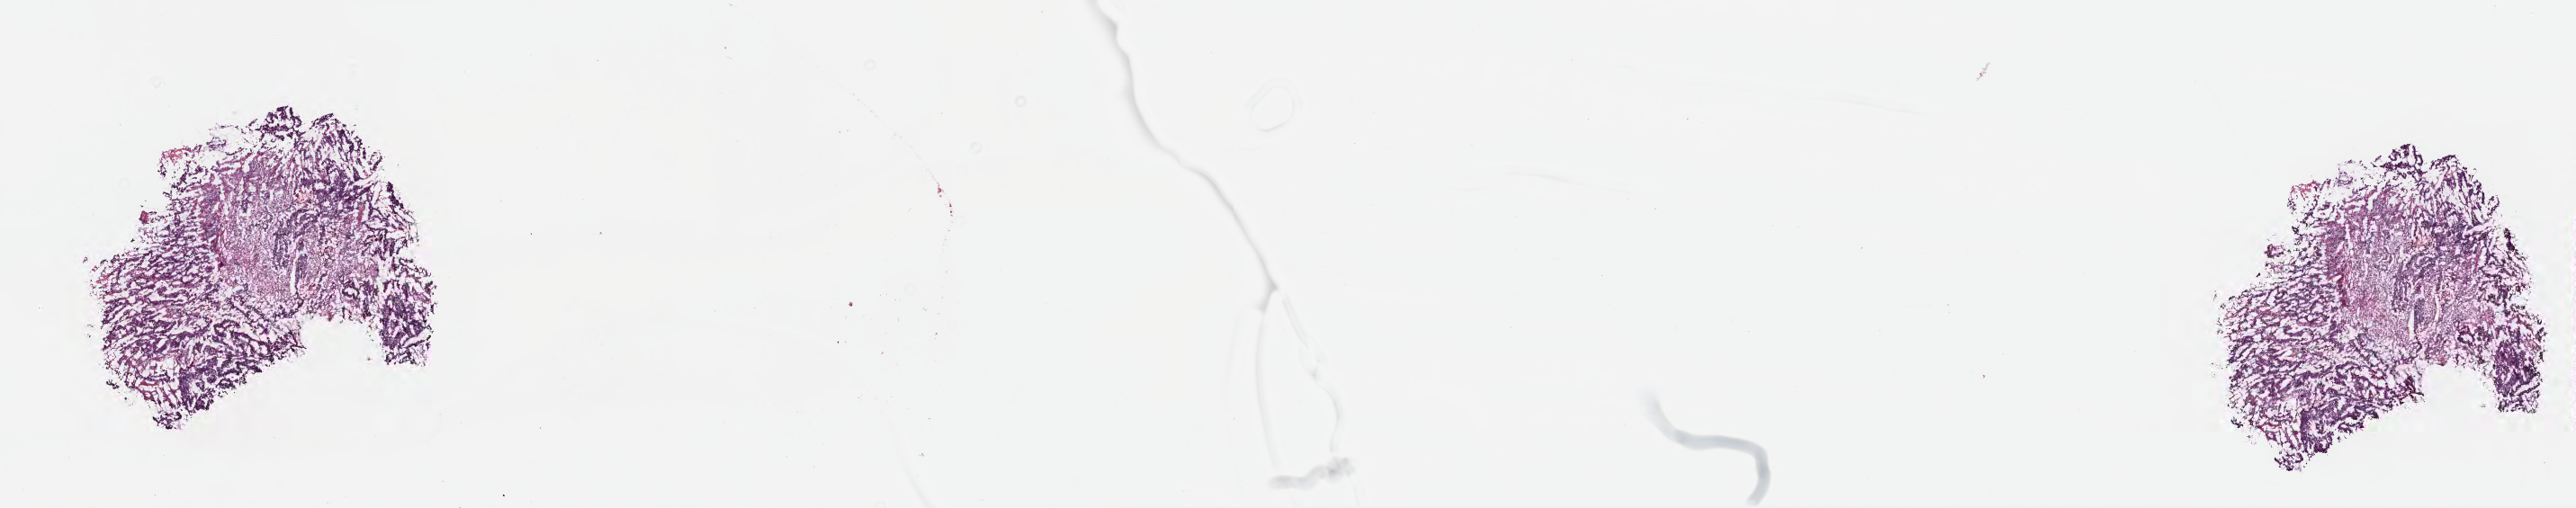
Digitized H&E-stained section — whole scanned area (about 23.1 x 4.6 mm) shown as a low-resolution overview, frozen section (tissue freezing medium), metastatic tumor tissue. Female patient; age at initial diagnosis 63 years. Composition of this section per pathologist review: tumor cells 70%, tumor nuclei 70%, stromal cells 20%, necrosis 0%, normal cells 10%. Inflammatory infiltration, as recorded: lymphocyte infiltration 8%, monocyte infiltration 0%, neutrophil infiltration 2%.
Section: bottom of the tissue portion. Patient diagnosis (primary): Adenocarcinoma, NOS.